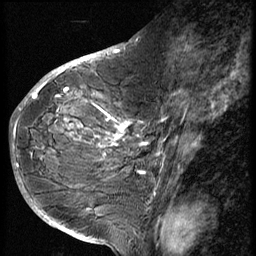
Breast MRI (dynamic contrast-enhanced), one sagittal slice; slice 28 of 56 in the series (ordered by position); 3 images stored at this slice position (order not interpretable as contrast timing); 1.5 T; TE 4.2 ms, TR 9 ms; 2.5 mm slice thickness; 256 × 256 image matrix, field of view 180 × 180 mm. Female patient, age 49 years. From the clinical record (not read from this slice): setting: breast cancer imaged before/during neoadjuvant chemotherapy; receptor status: HER2-positive.
Structures marked on this image (semi-automatic segmentation, software-assisted and operator-edited):
- analysis volume of interest (the breast-tissue region the enhancement analysis was run in; not a lesion): bounding box <37,85,132,207> (left, top, right, bottom; pixels)
- tumour enhancement mask (voxels above the 140 % enhancement threshold inside the analysis volume of interest): <37,85,130,156>